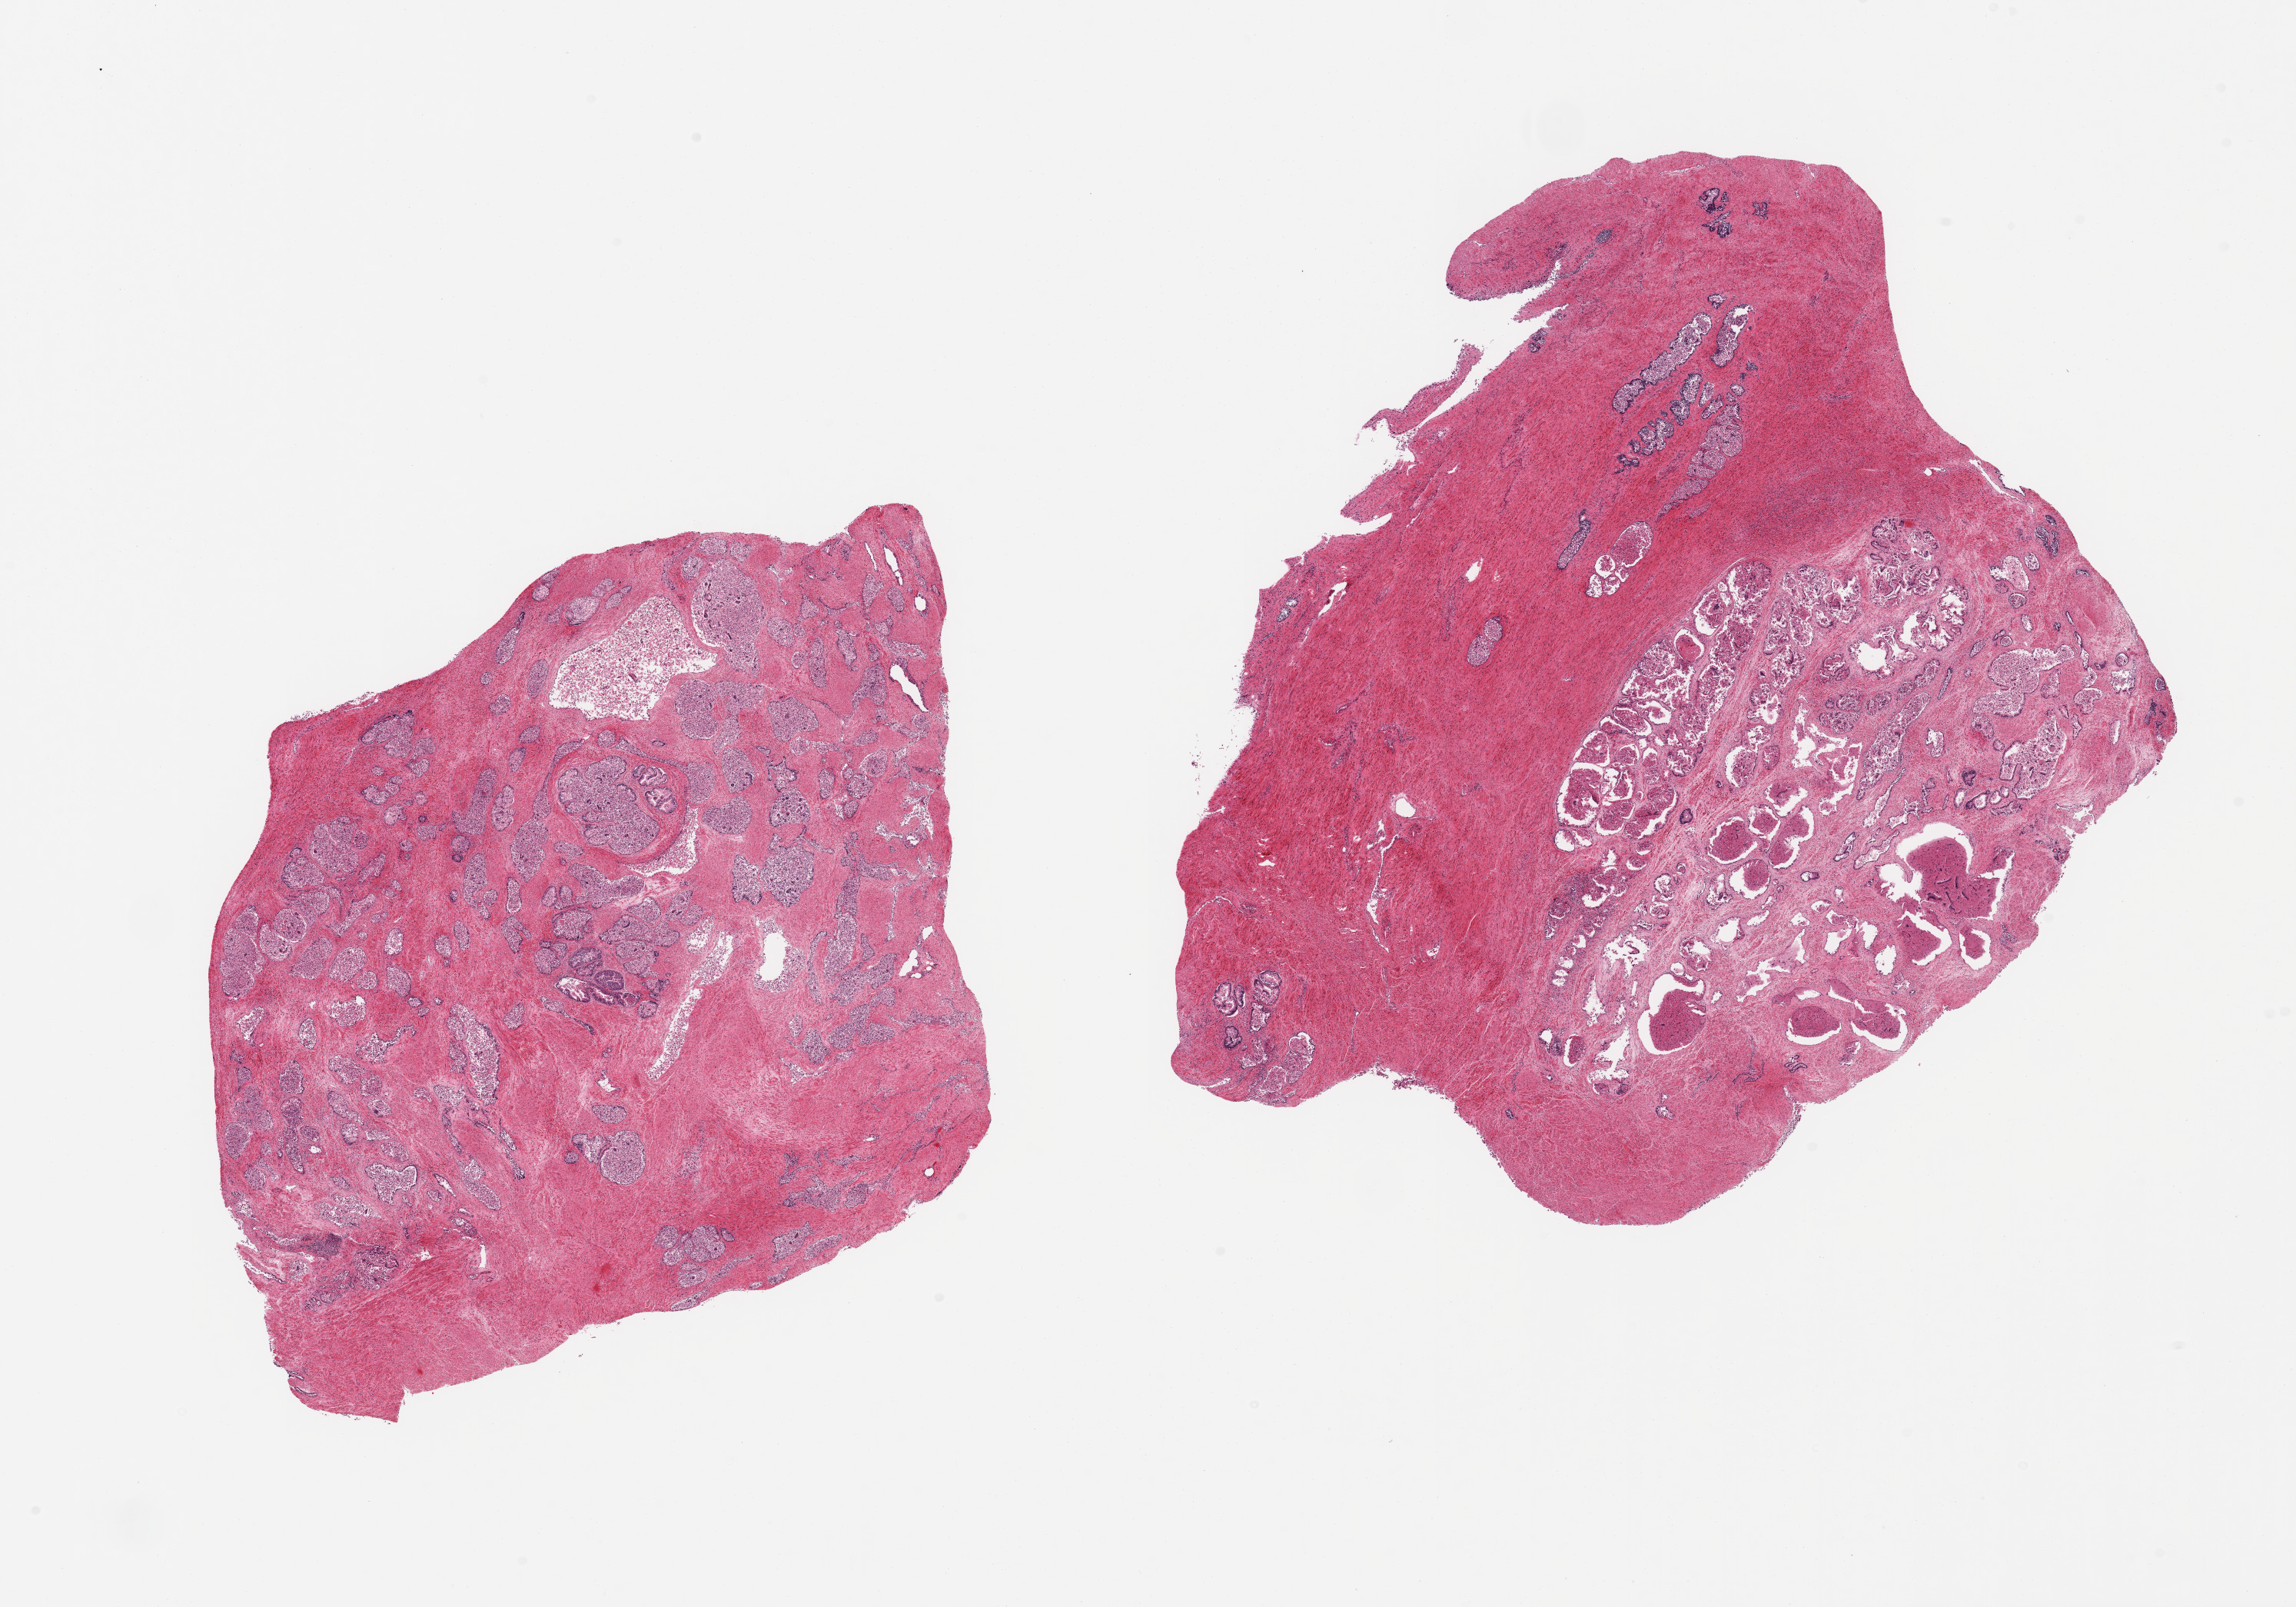
H&E whole-slide image, shown as a low-resolution overview of the whole scanned area (about 23.6 x 16.5 mm); PAXgene-fixed, paraffin-embedded tissue; section of prostate (target tissue); tissue donor sample. Donor sex: male.
Reviewer comment on this tissue sample: 2 pieces, glandular mucosa with advanced autolysis; hyperplastic pattern.